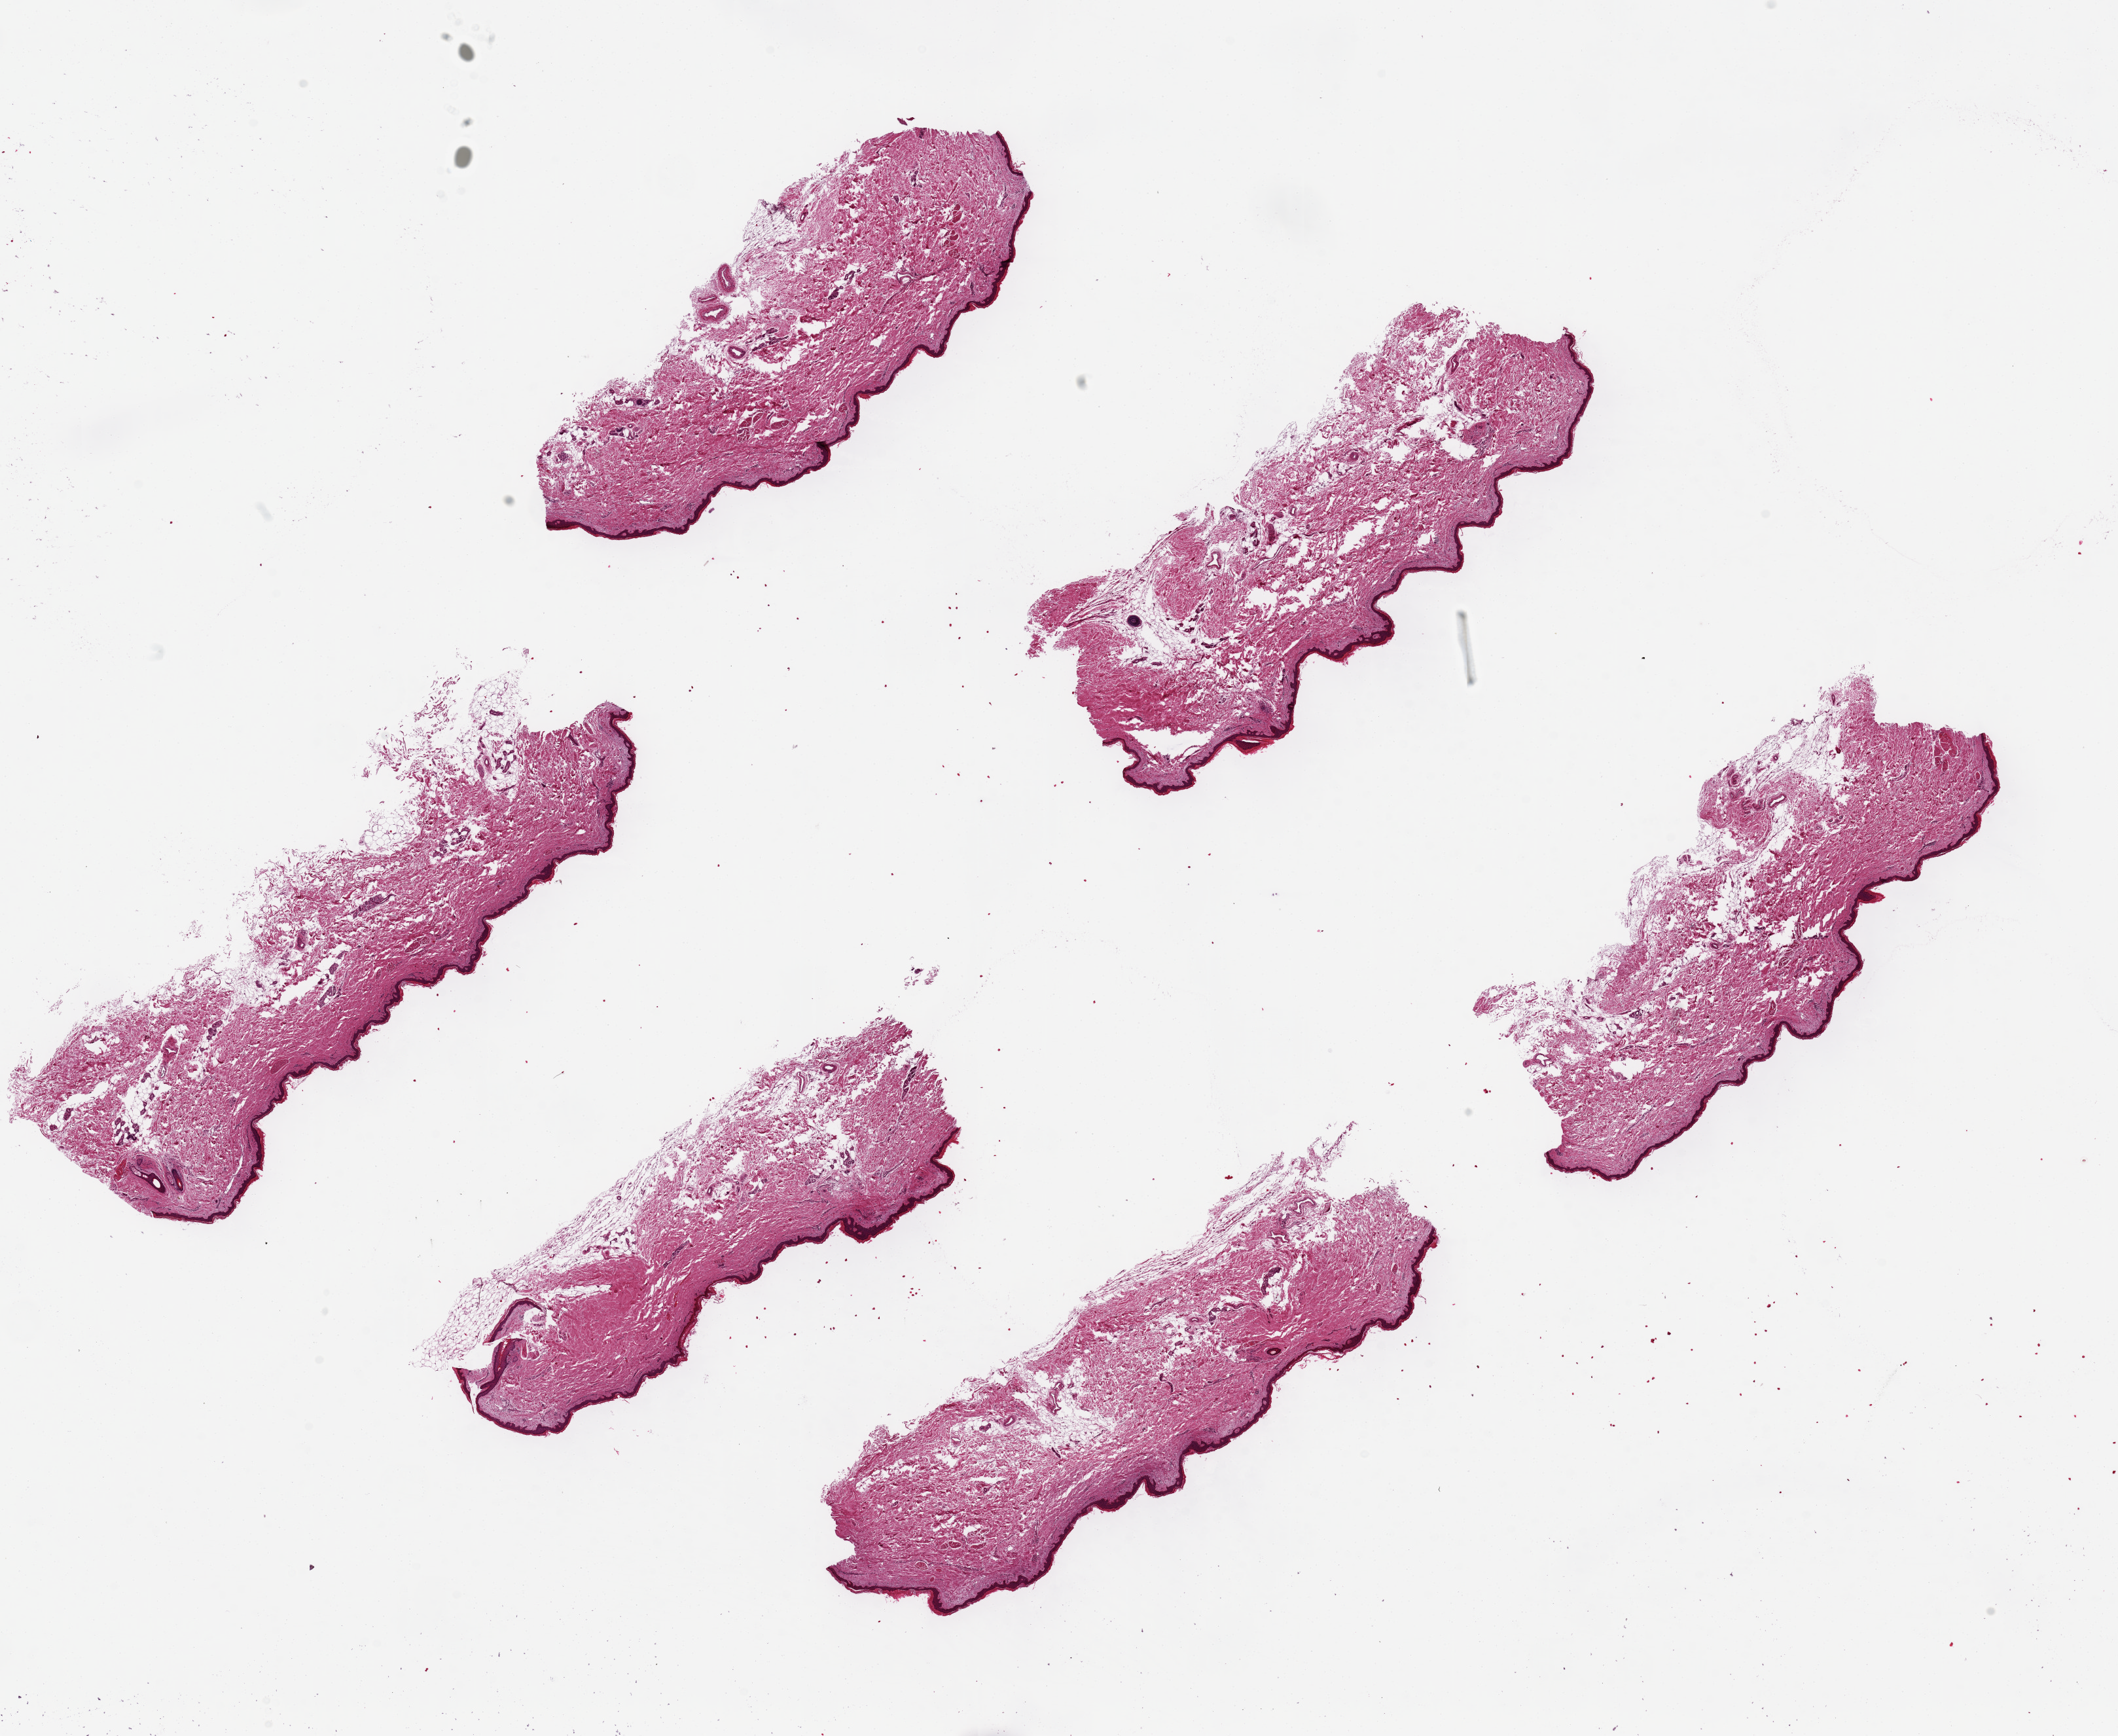
Whole-slide image, haematoxylin and eosin stain — whole scanned area (about 25.6 x 21.0 mm, from a 20x scan) shown as a low-resolution overview; PAXgene-fixed paraffin-embedded (PFPE) section; target tissue: skin of lower leg; tissue donor sample. Male donor.
Pathologist's review note for this sample: 6 pieces. Squamous epithelium is -2-3% of thickness.